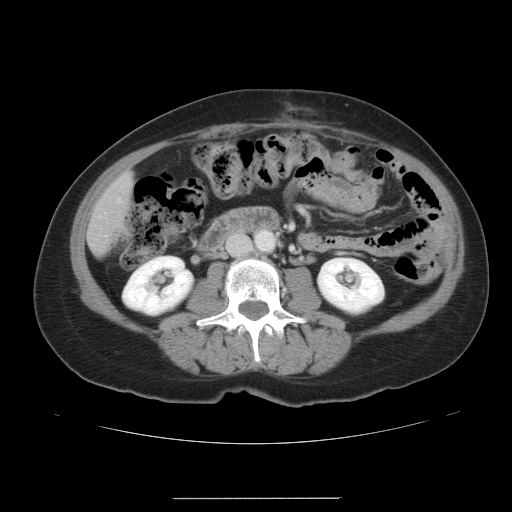
Contrast-enhanced abdominal CT, one axial slice. Position 9 of 41 along the scan axis. 120 kVp. Intravenous contrast given. Soft-tissue window (W 400 / L 40 HU). 512 × 512 image matrix, field of view 381 × 381 mm. Female patient, age 63 years. From the clinical record (not read from this slice): diagnosis: colorectal cancer liver metastases, imaged before liver resection; multiple liver metastases: yes.
Outlined on this slice (expert manual segmentation):
- liver: bounding box <89,176,134,252> (left, top, right, bottom; pixels)
- planned liver remnant (the part of the liver to remain after resection): <89,176,134,252>